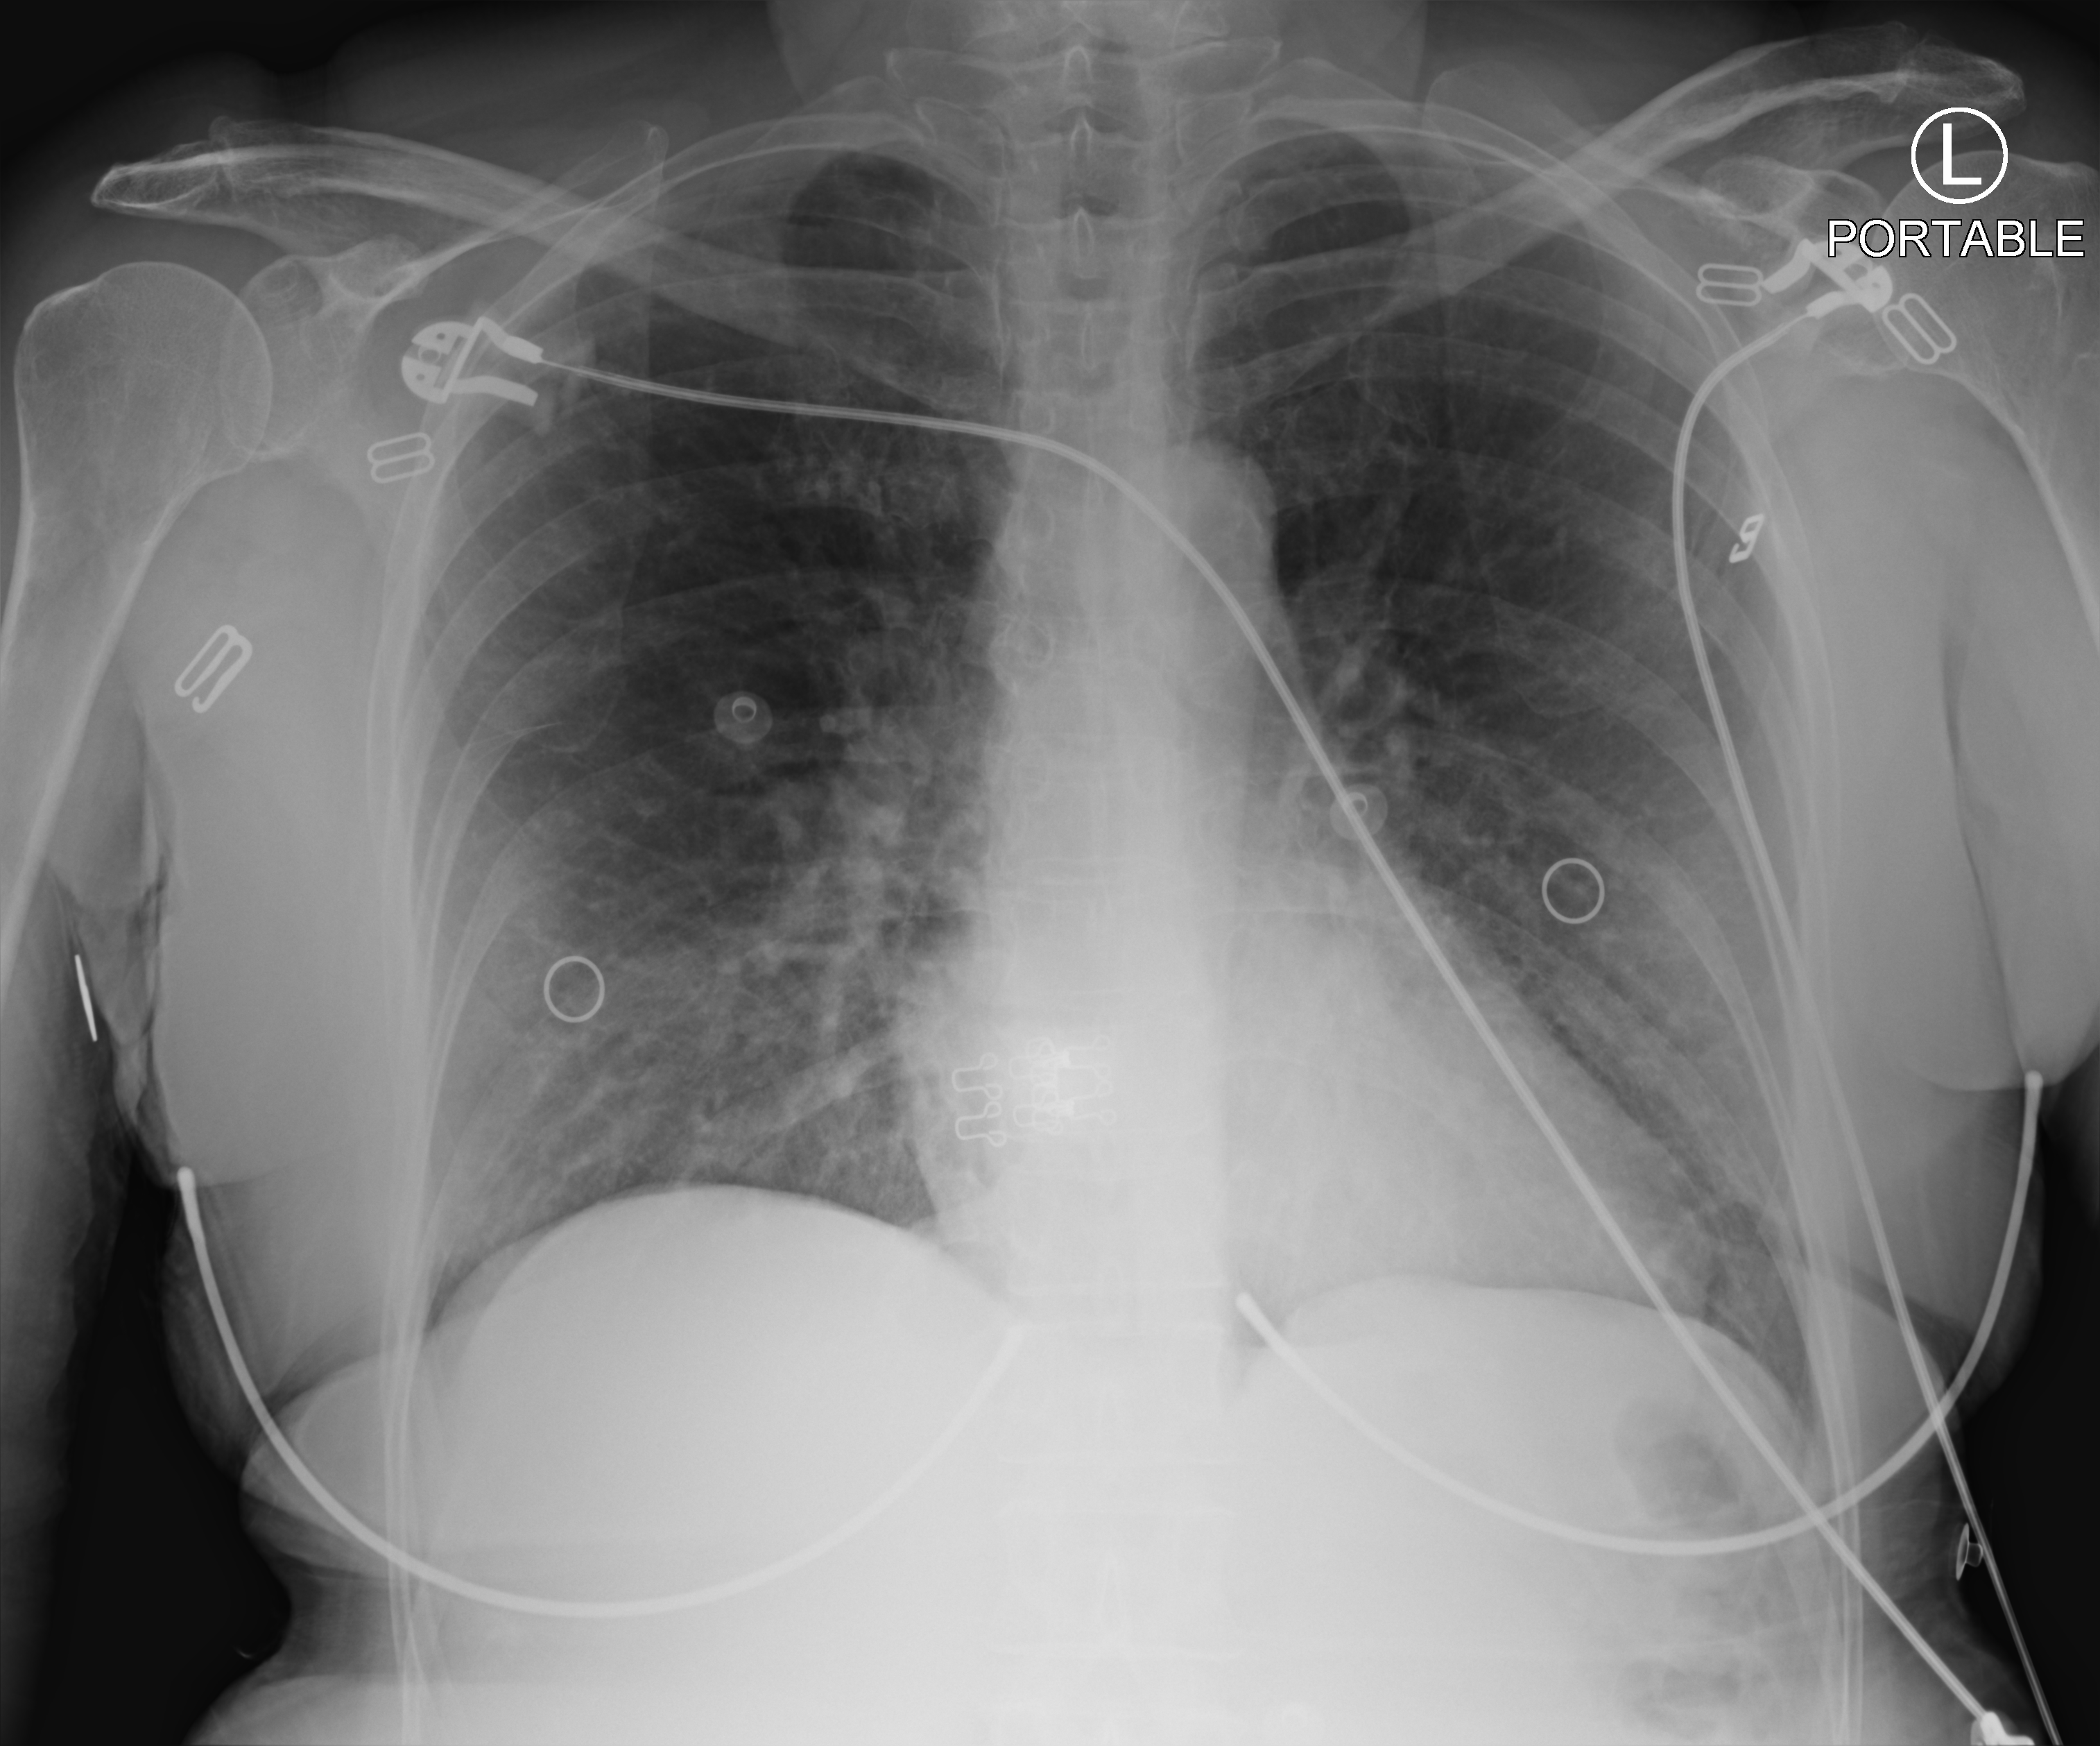
Chest X-ray (portable), anteroposterior (AP) projection. Female patient hospitalised with COVID-19, age 60–74 years.
From the hospital-stay record, not from the radiograph (when in the stay this image was taken is not recorded): length of hospital stay: 1 day; mechanically ventilated during this hospital stay: no; admitted to intensive care during this hospital stay: no.